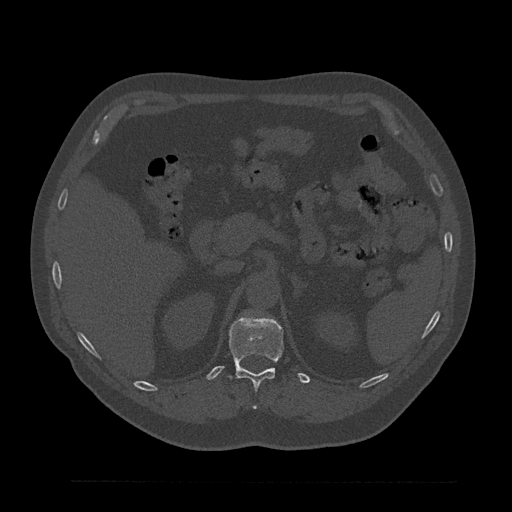
CT including the spine, one axial slice. Reconstruction kernel Br40s/3. 120 kVp. Bone window (W 1800 / L 400 HU). 0.5 mm slice thickness. 512 × 512 image matrix, field of view 430 × 430 mm. Male patient, age 61 years. Case-level facts recorded for this patient, not image findings: primary cancer: prostate.
Annotated regions visible in this slice (semi-automatically segmented with operator editing):
- T12 vertebra: bounding box [x1, y1, x2, y2] px = [229, 316, 284, 408]